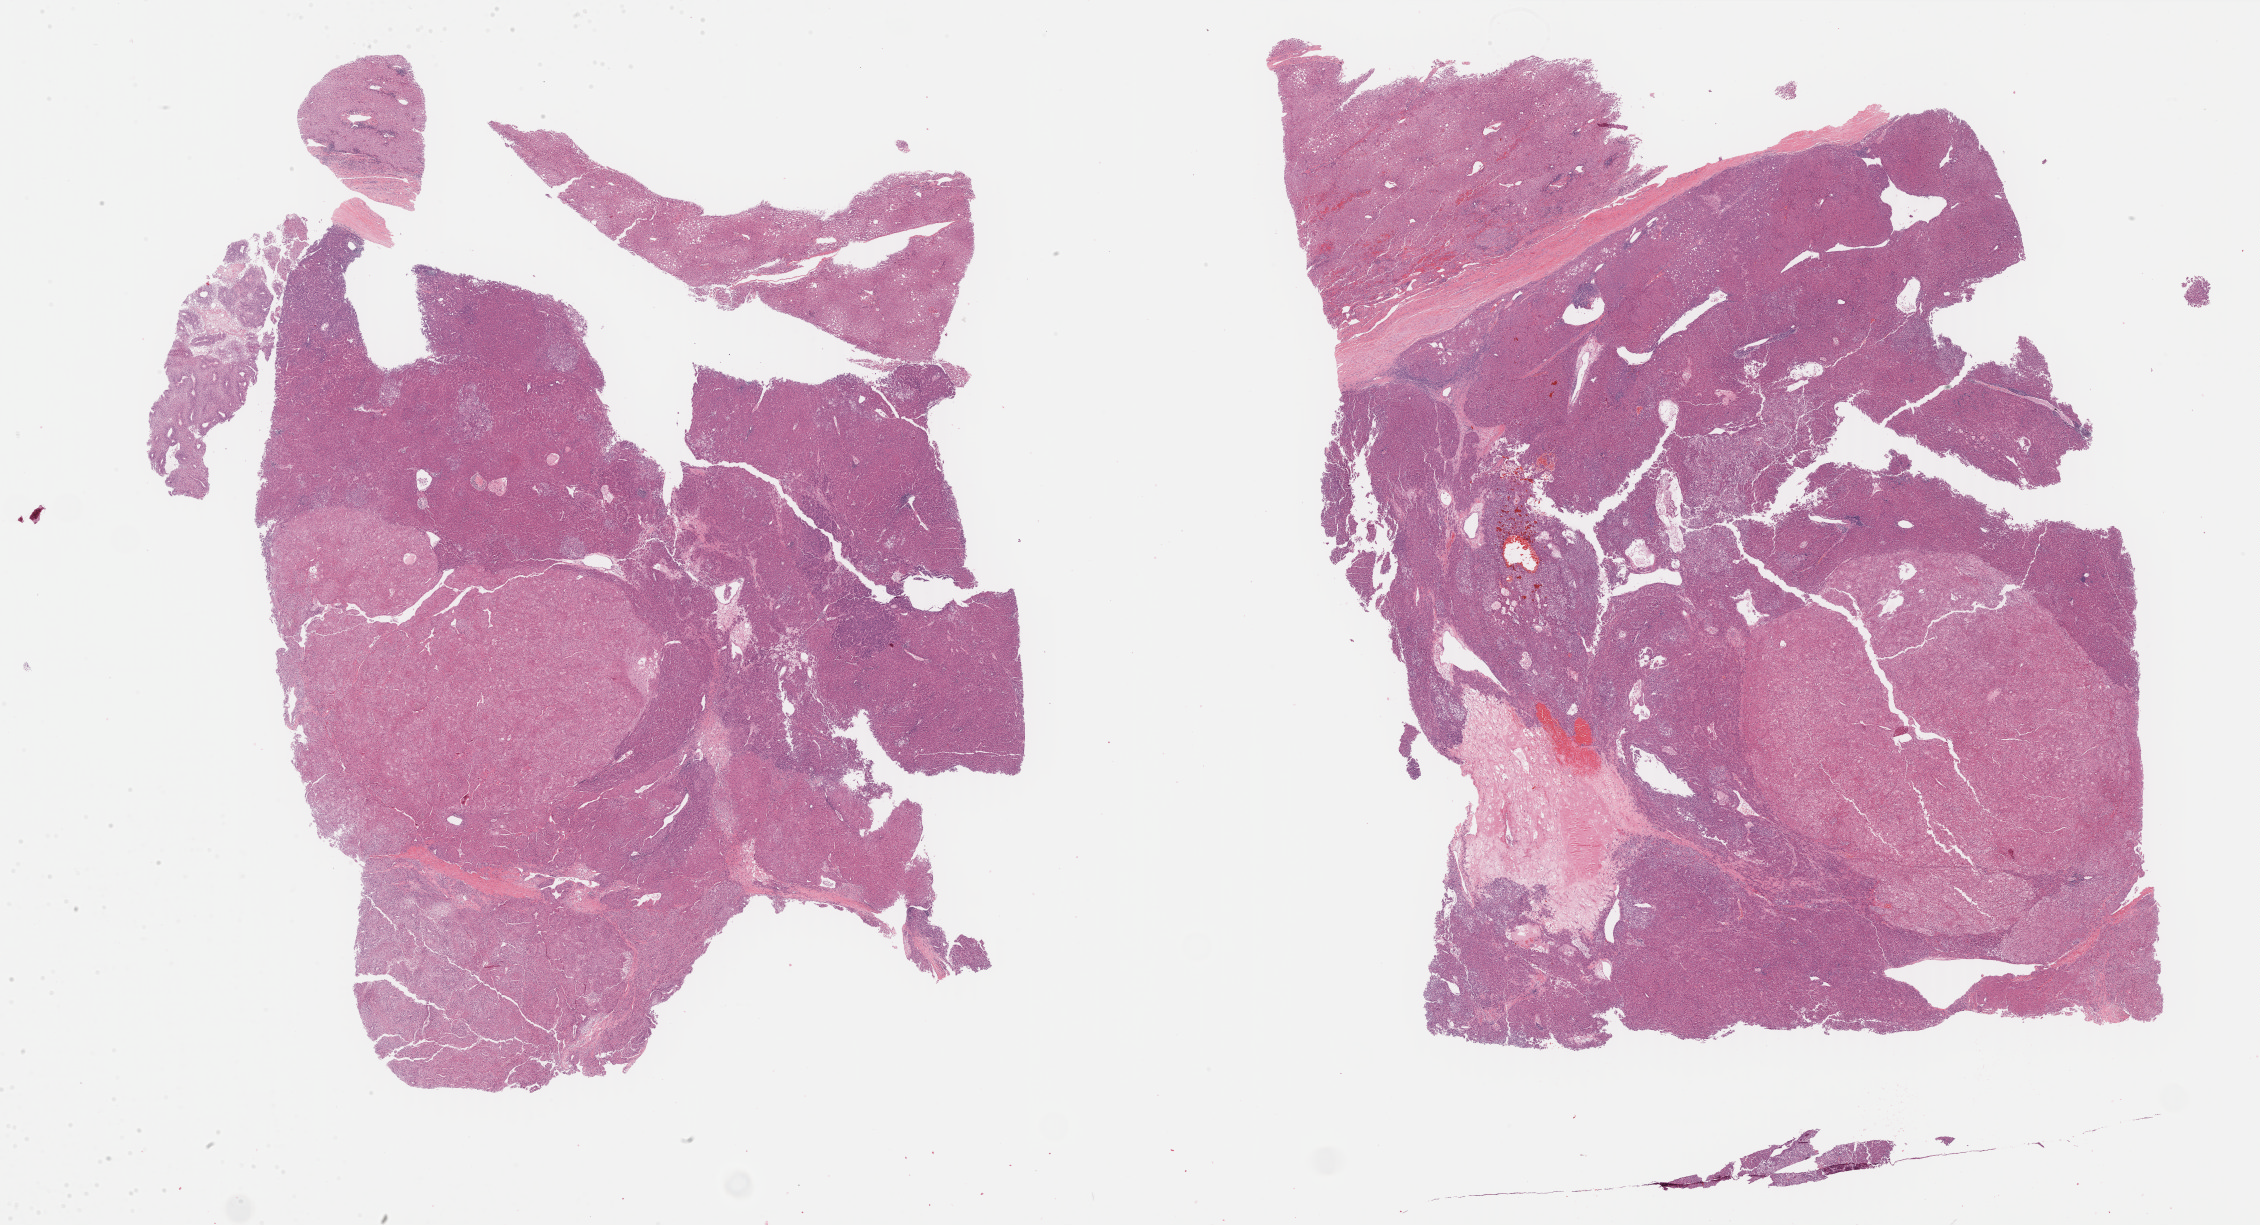
H&E whole-slide image — whole scanned area (about 36.6 x 19.8 mm, acquisition: 40x scan) shown as a low-resolution overview. Formalin-fixed paraffin-embedded (FFPE) diagnostic section. Sample: primary tumour, liver. Male, age 77 years at initial diagnosis. Histologic grade: G2 (moderately differentiated).
• histologic diagnosis: Hepatocellular carcinoma, NOS
• TNM: T3a NX M0
• AJCC pathologic stage: IIIA (7th edition)